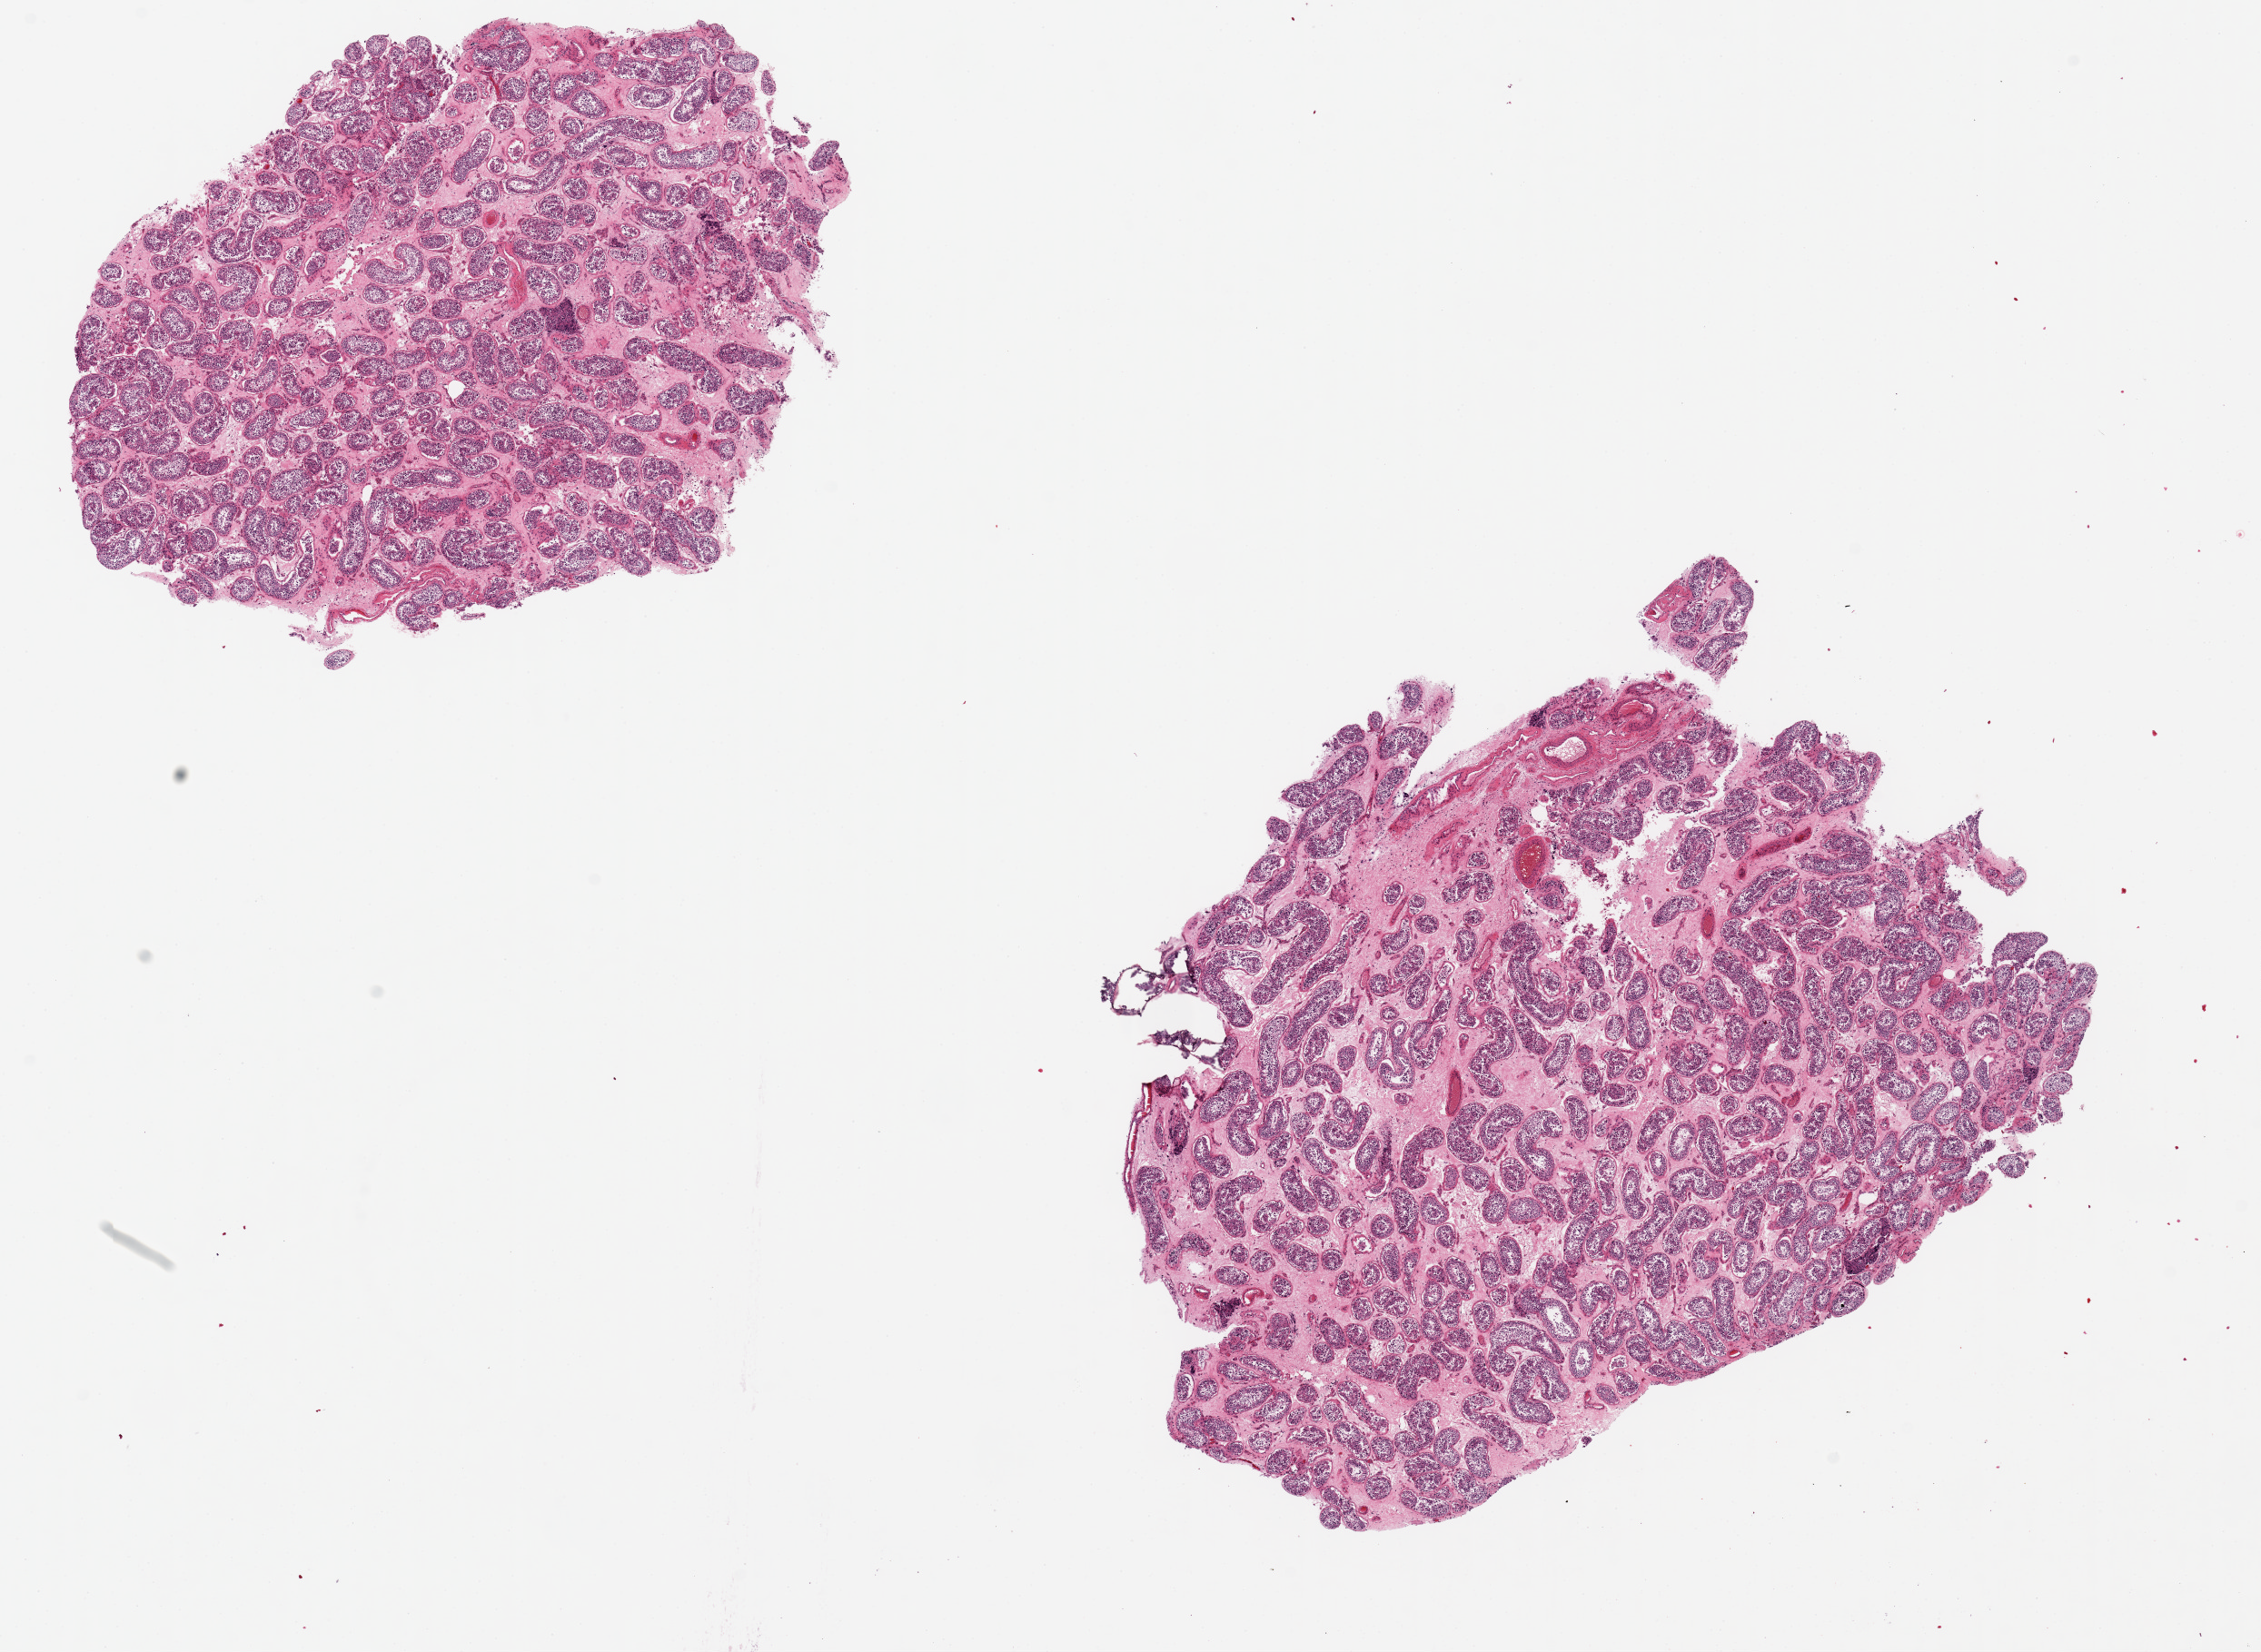
Digitized haematoxylin and eosin-stained section, brightfield — low-resolution overview of the scanned area, about 19.7 x 14.4 mm; PAXgene-fixed, paraffin-embedded tissue; section of testis (target tissue); donor tissue sample.
Review note (as recorded): 2 pieces, 7x6 & 9x7mm; spermatogenesis present.